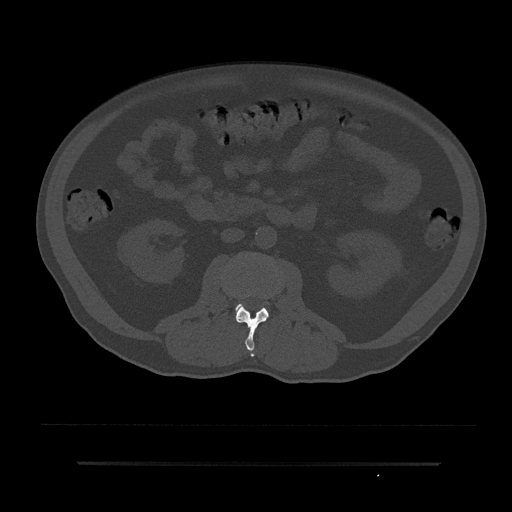
CT including the spine, one axial slice. Position 47 of 797 along the scan axis. Reconstruction kernel Br40s/3. 120 kVp. Bone window (W 1800 / L 400 HU). 0.5 mm slice thickness. 512 × 512 image matrix, field of view 464 × 464 mm. Male patient, age 59 years. From the clinical record (not read from this slice): primary cancer: bile ducts.
Outlined on this slice (semi-automatically segmented with operator editing):
- L2 vertebra: box from (x=236, y=290) to (x=269, y=357) px